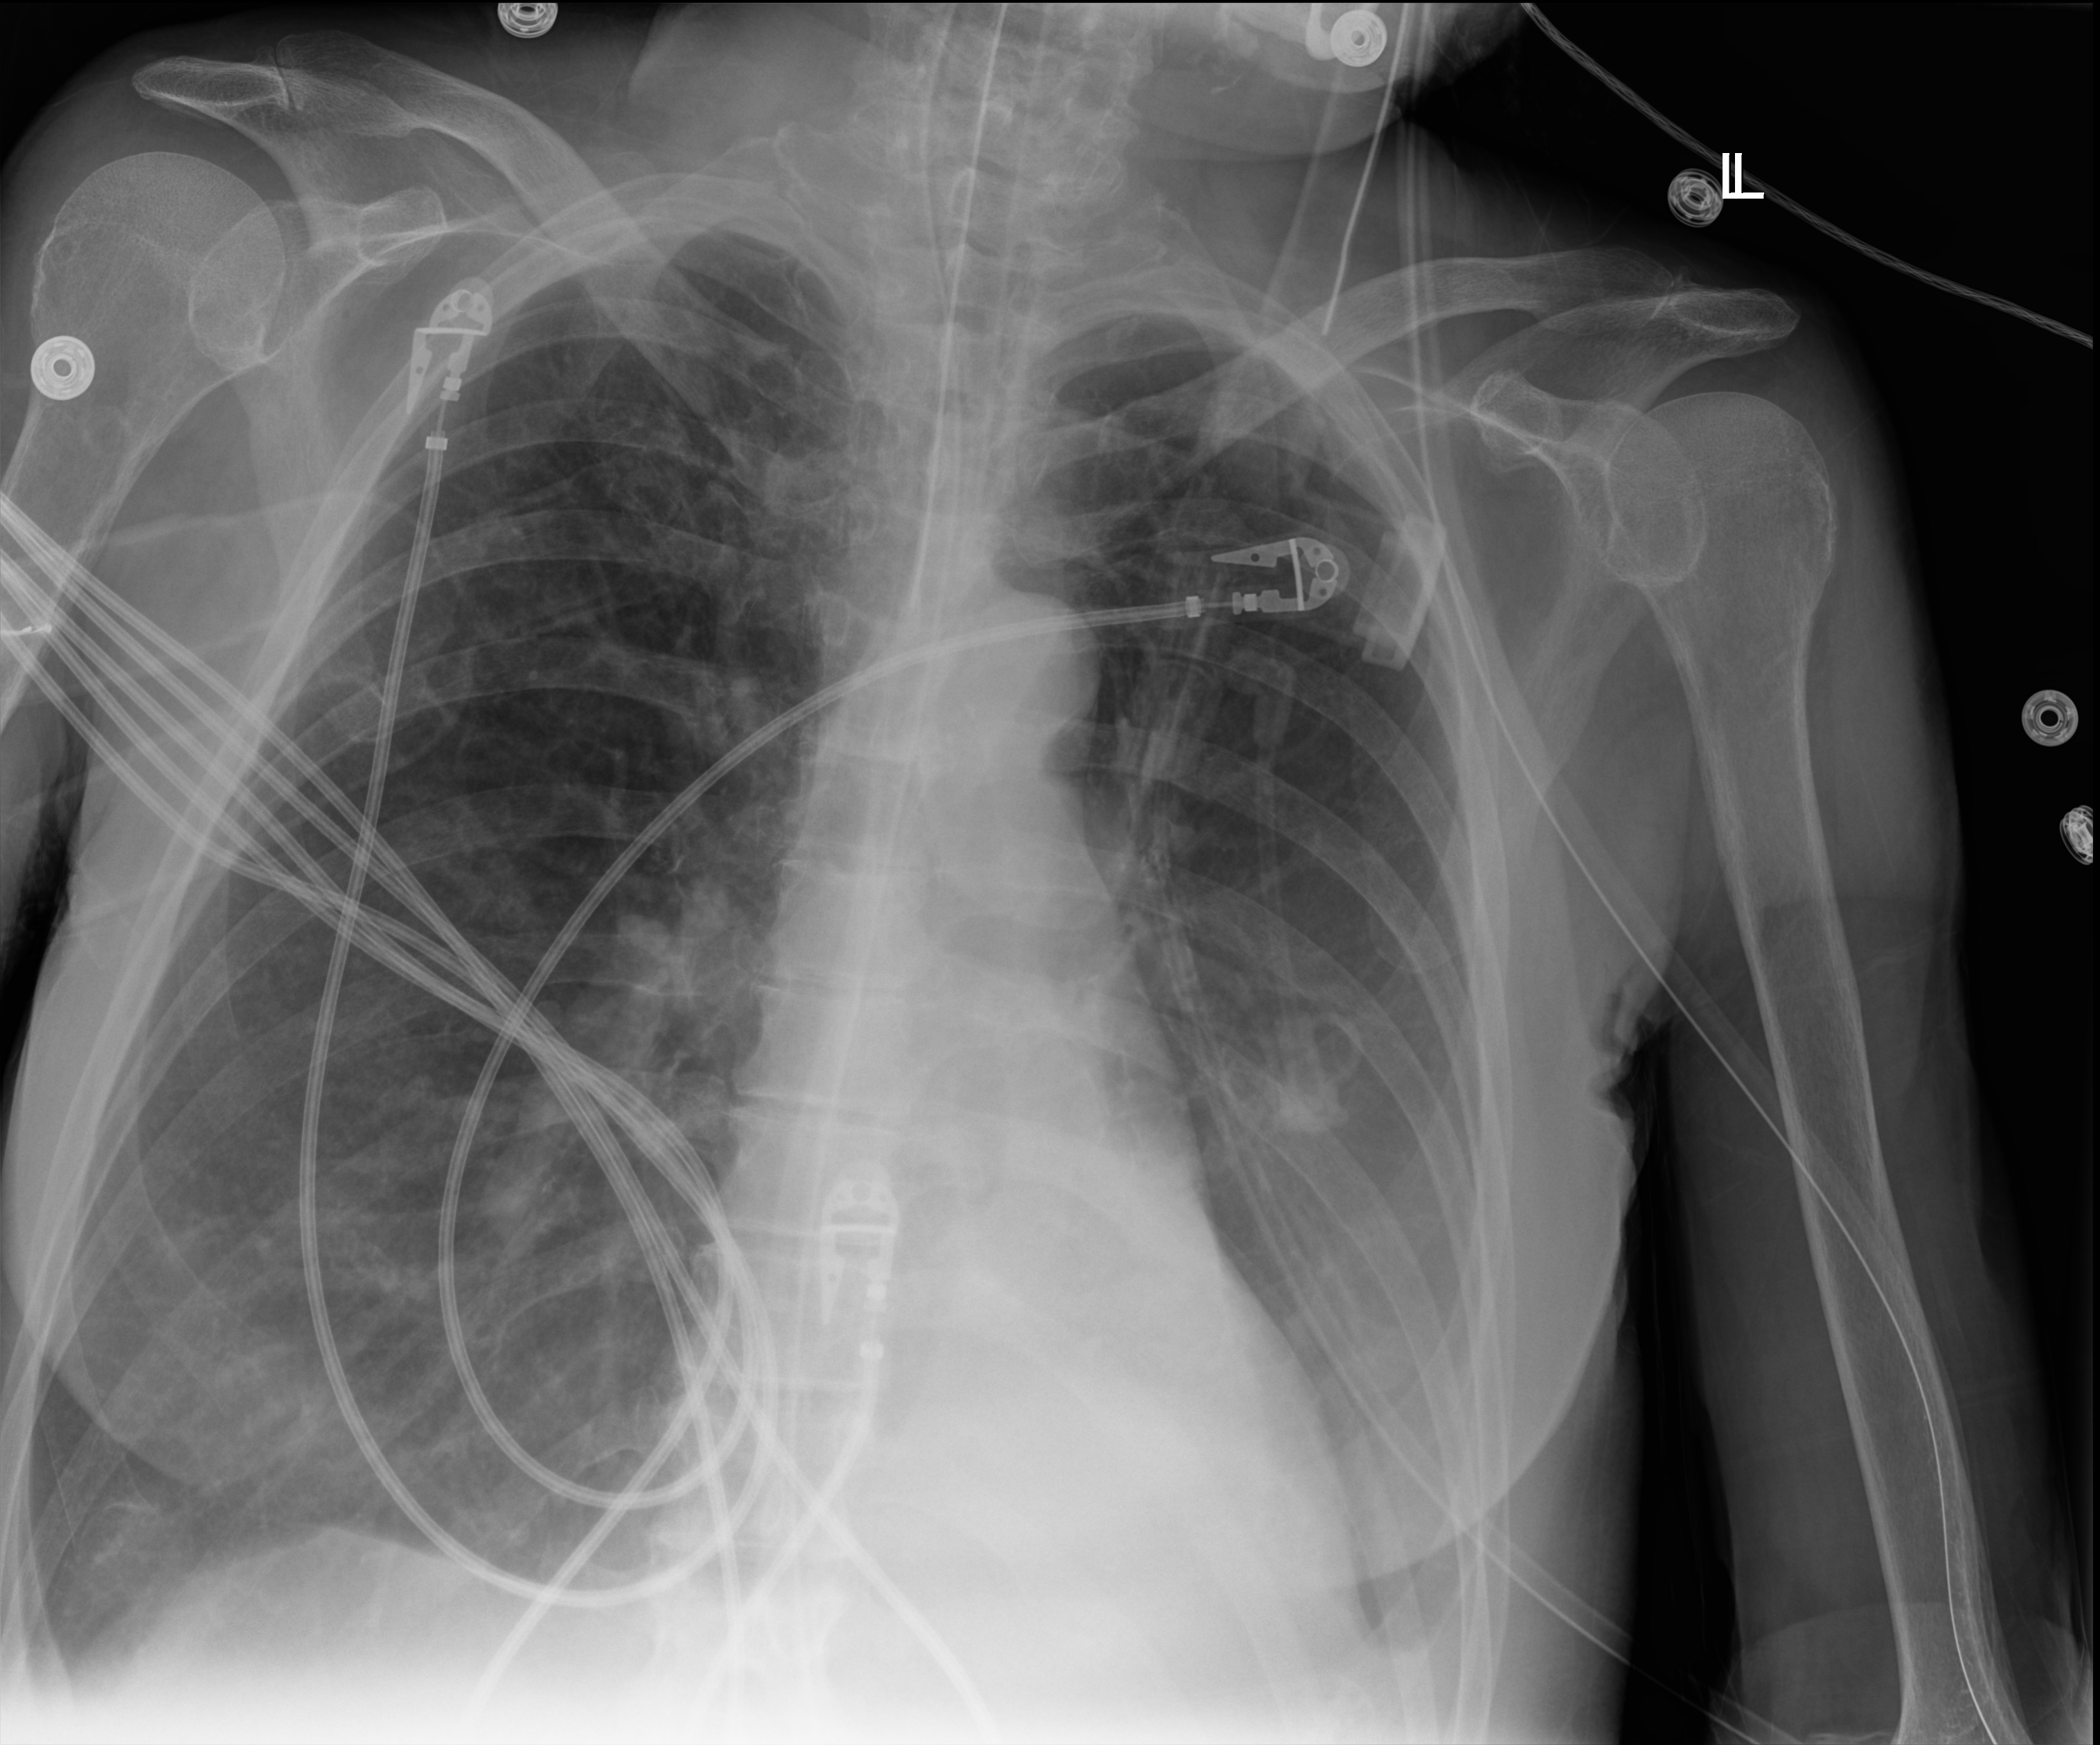
Portable chest radiograph; anteroposterior (AP) projection. Patient hospitalised with COVID-19; female, aged 60–74 years.
Hospital-stay facts (about this admission, not read from this image; timing relative to this image not recorded):
- admitted to intensive care during this hospital stay: yes
- mechanically ventilated during this hospital stay: yes